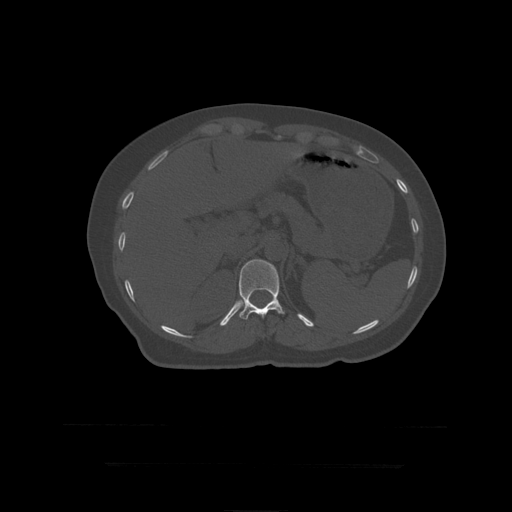
CT including the spine, one axial slice; position 199 of 399 along the scan axis; 120 kVp; bone window (W 1800 / L 400 HU); 1.25 mm slice thickness; 512 × 512 image matrix, field of view 450 × 450 mm. Patient age 41 years. Case-level facts recorded for this patient, not image findings: primary cancer: breast.
Structures marked on this image (semi-automatic segmentation, software-assisted and operator-edited):
- T12 vertebra: bounding box (x1, y1, x2, y2) in pixels: (239, 260, 285, 320)